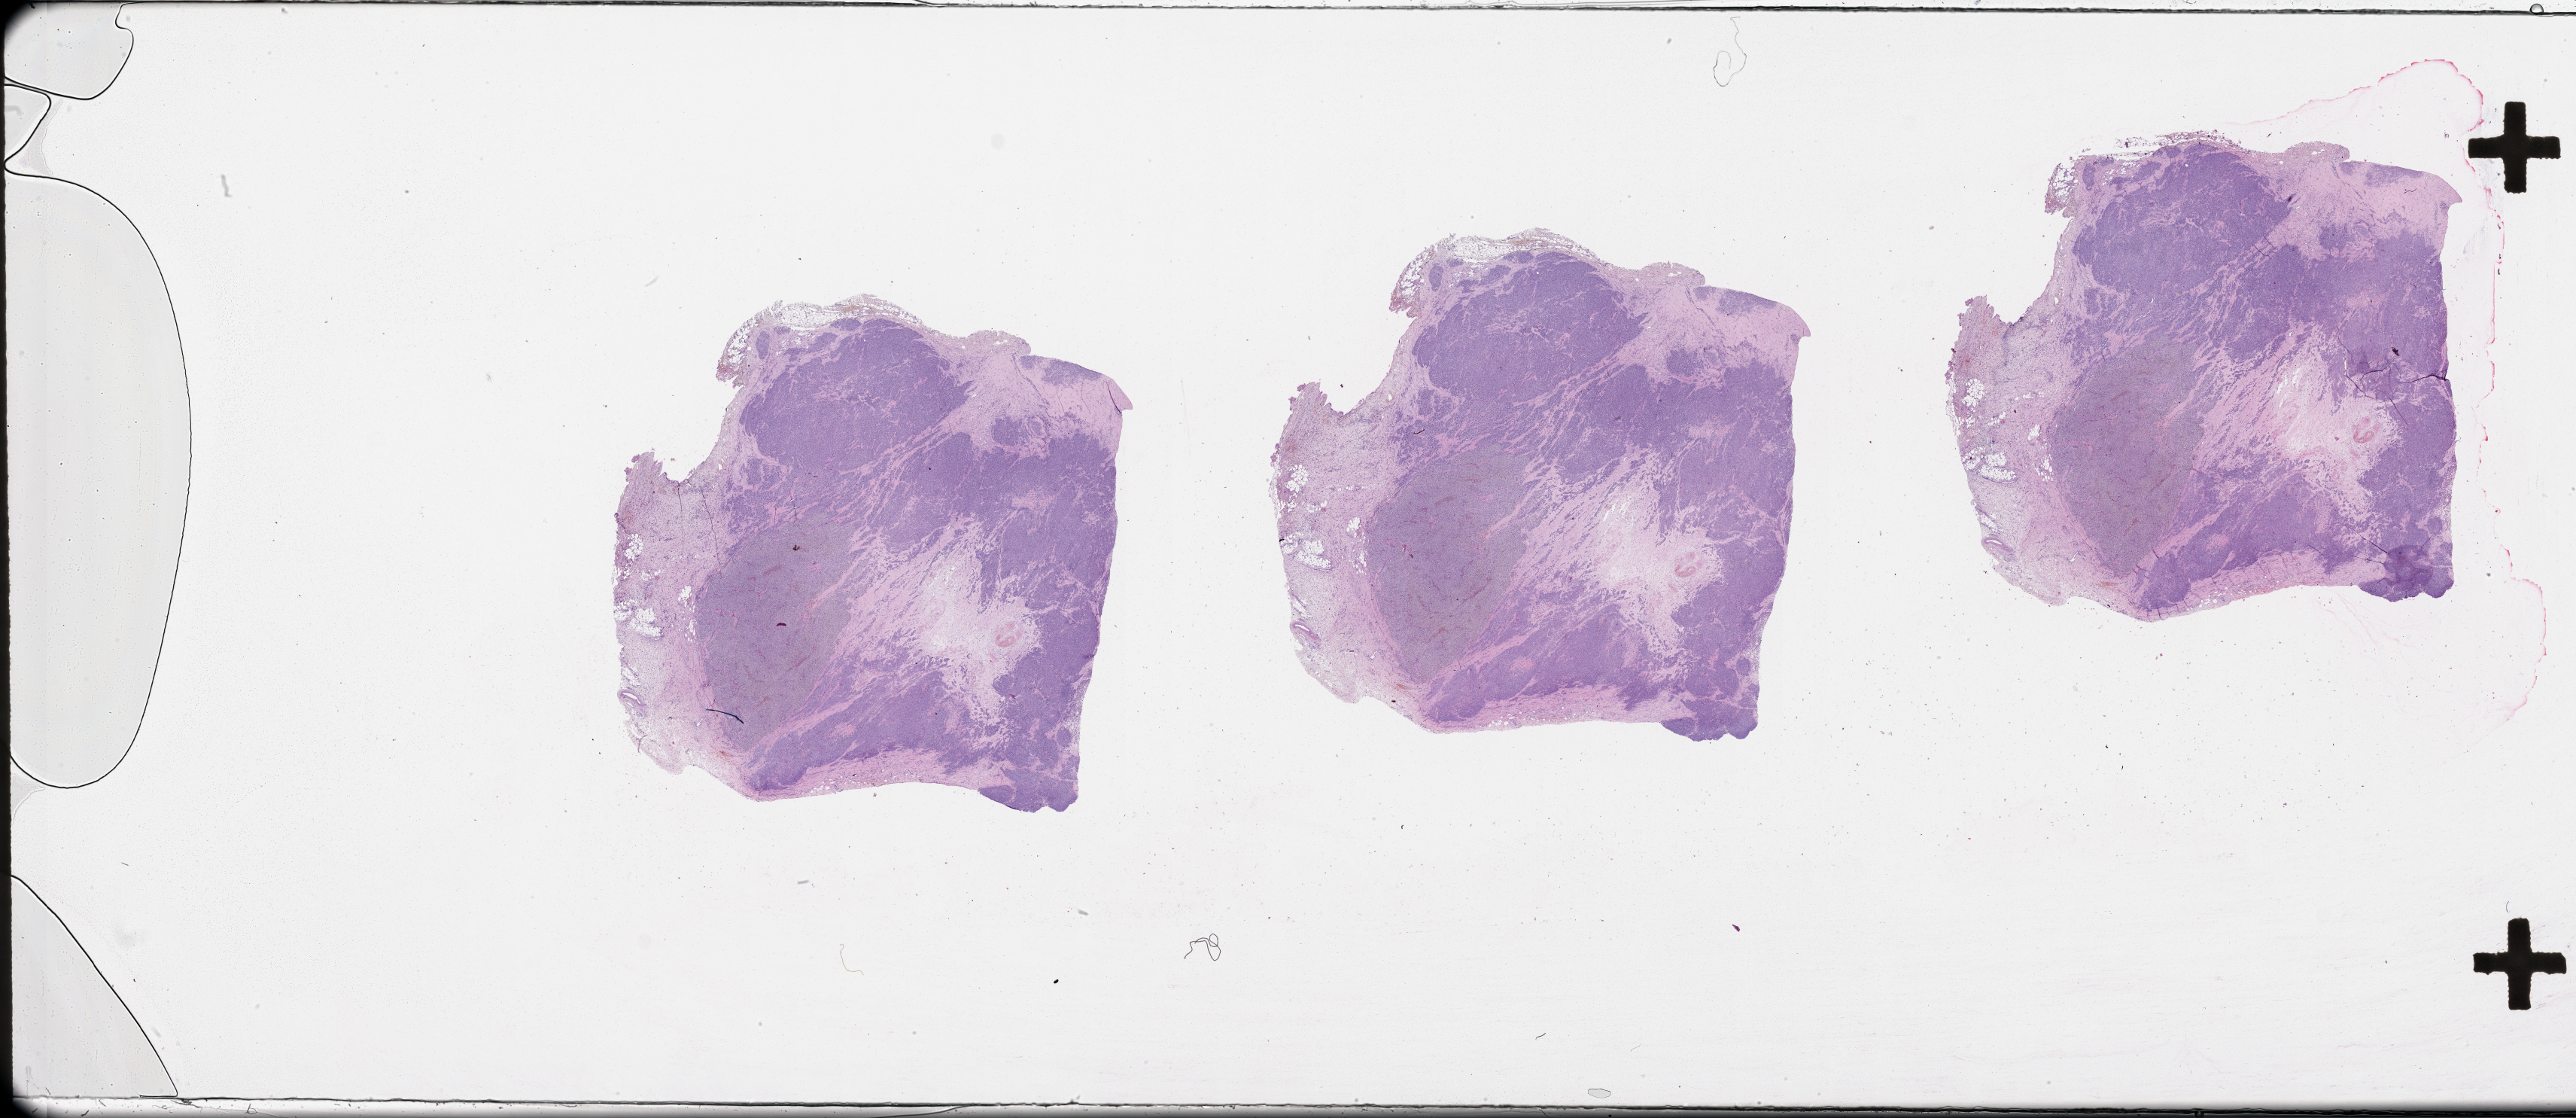
Digitized H&E tissue section (whole slide), low-resolution overview of the scanned area, about 55.1 x 23.9 mm. Male, 83 y/o.
Patient diagnosis: Malignant melanoma, NOS.